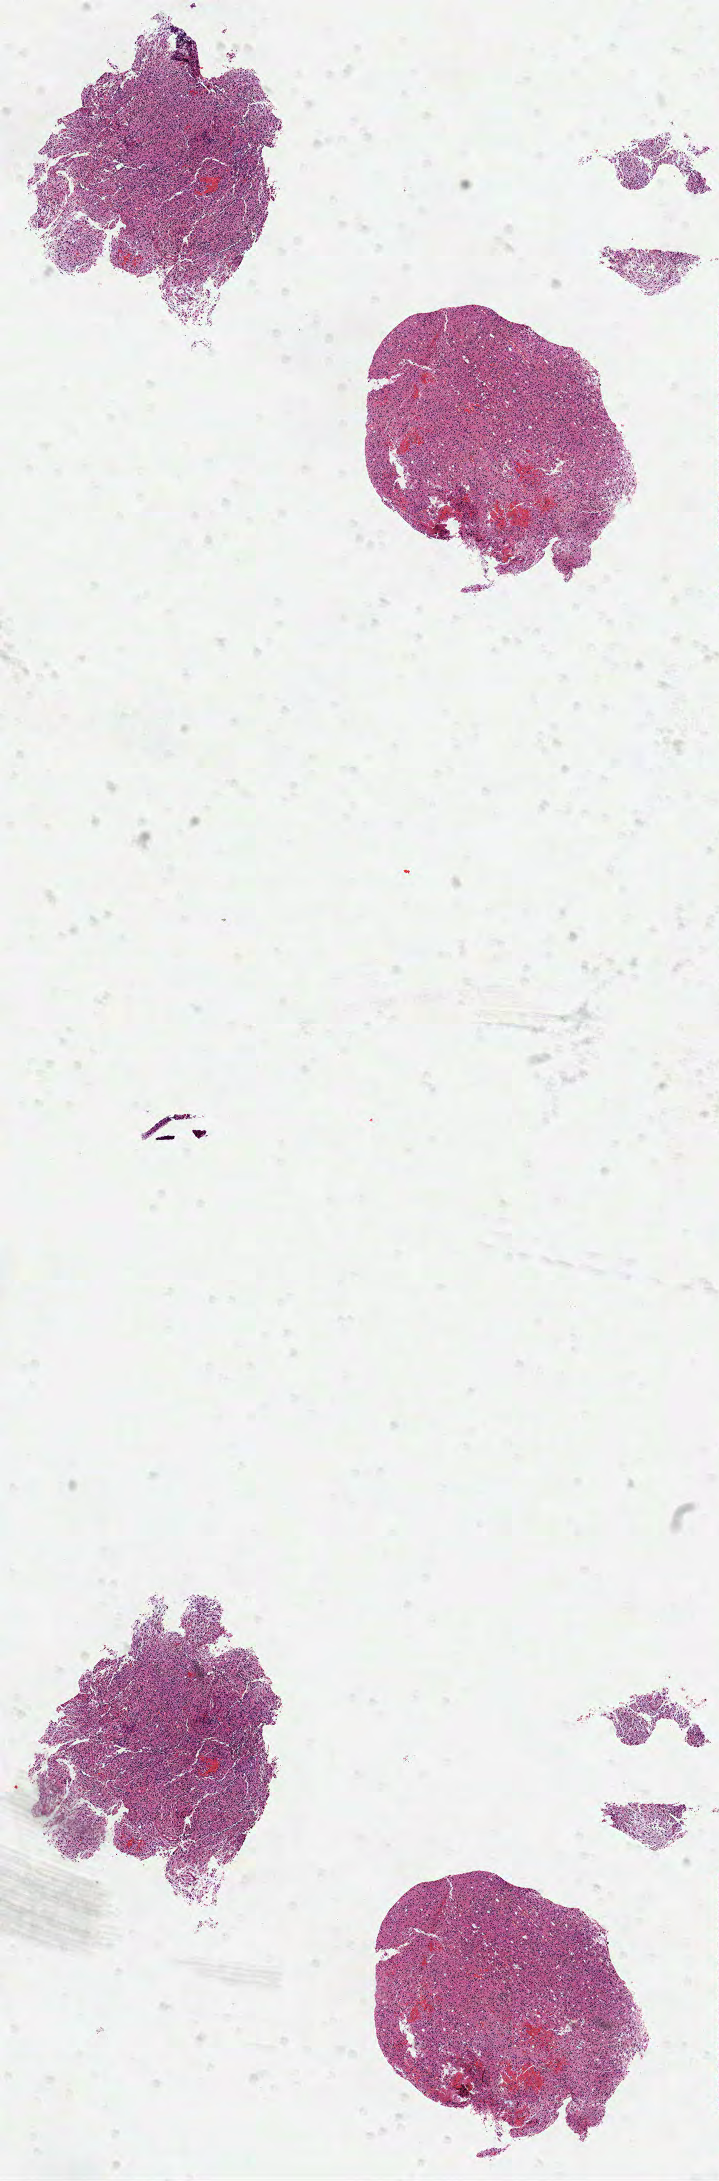
Hematoxylin and eosin (H&E) stained whole-slide image, a low-resolution overview of the entire scanned area, about 5.8 x 17.6 mm (slide scanned at 40x); formalin-fixed paraffin-embedded (FFPE) diagnostic section; sample: primary tumour, brain. Male patient; age at initial diagnosis 43 years. Histologic grade: G2 (moderately differentiated).
- pathologic diagnosis: Oligodendroglioma, NOS (cerebrum)